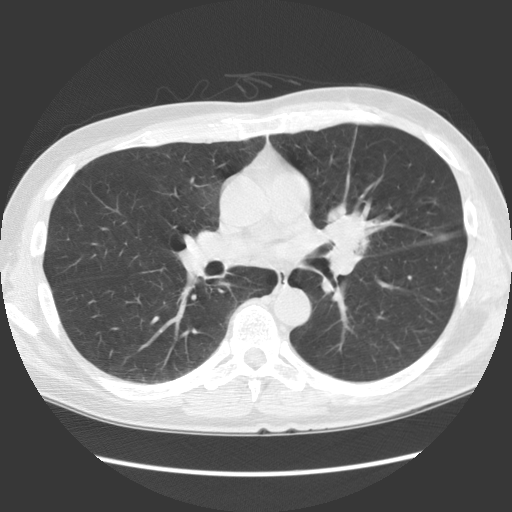
Axial slice from a low-dose chest CT screening exam, baseline annual screen, lung window (W 1500 / L -600 HU), 2.5 mm slice thickness, slice 72 of 136 in the series, 512 × 512 image matrix. Male, age 61 years at enrolment. Former smoker at enrolment.
• Expert reader's lesion annotation, bounding box <292,195,390,296> (left, top, right, bottom; pixels).
• Reader record for this screening exam (exam-level; its link to the box is not recorded): non-calcified nodule or mass ≥4 mm, lingula, 35 × 35 mm, spiculated (stellate) margins, soft tissue attenuation.
• Participant outcome: lung cancer diagnosed 58 days after this screen — squamous cell carcinoma, NOS, left hilum, left main stem bronchus, poorly differentiated (G3), stage IA (AJCC 6th edition), 40 mm at pathology.